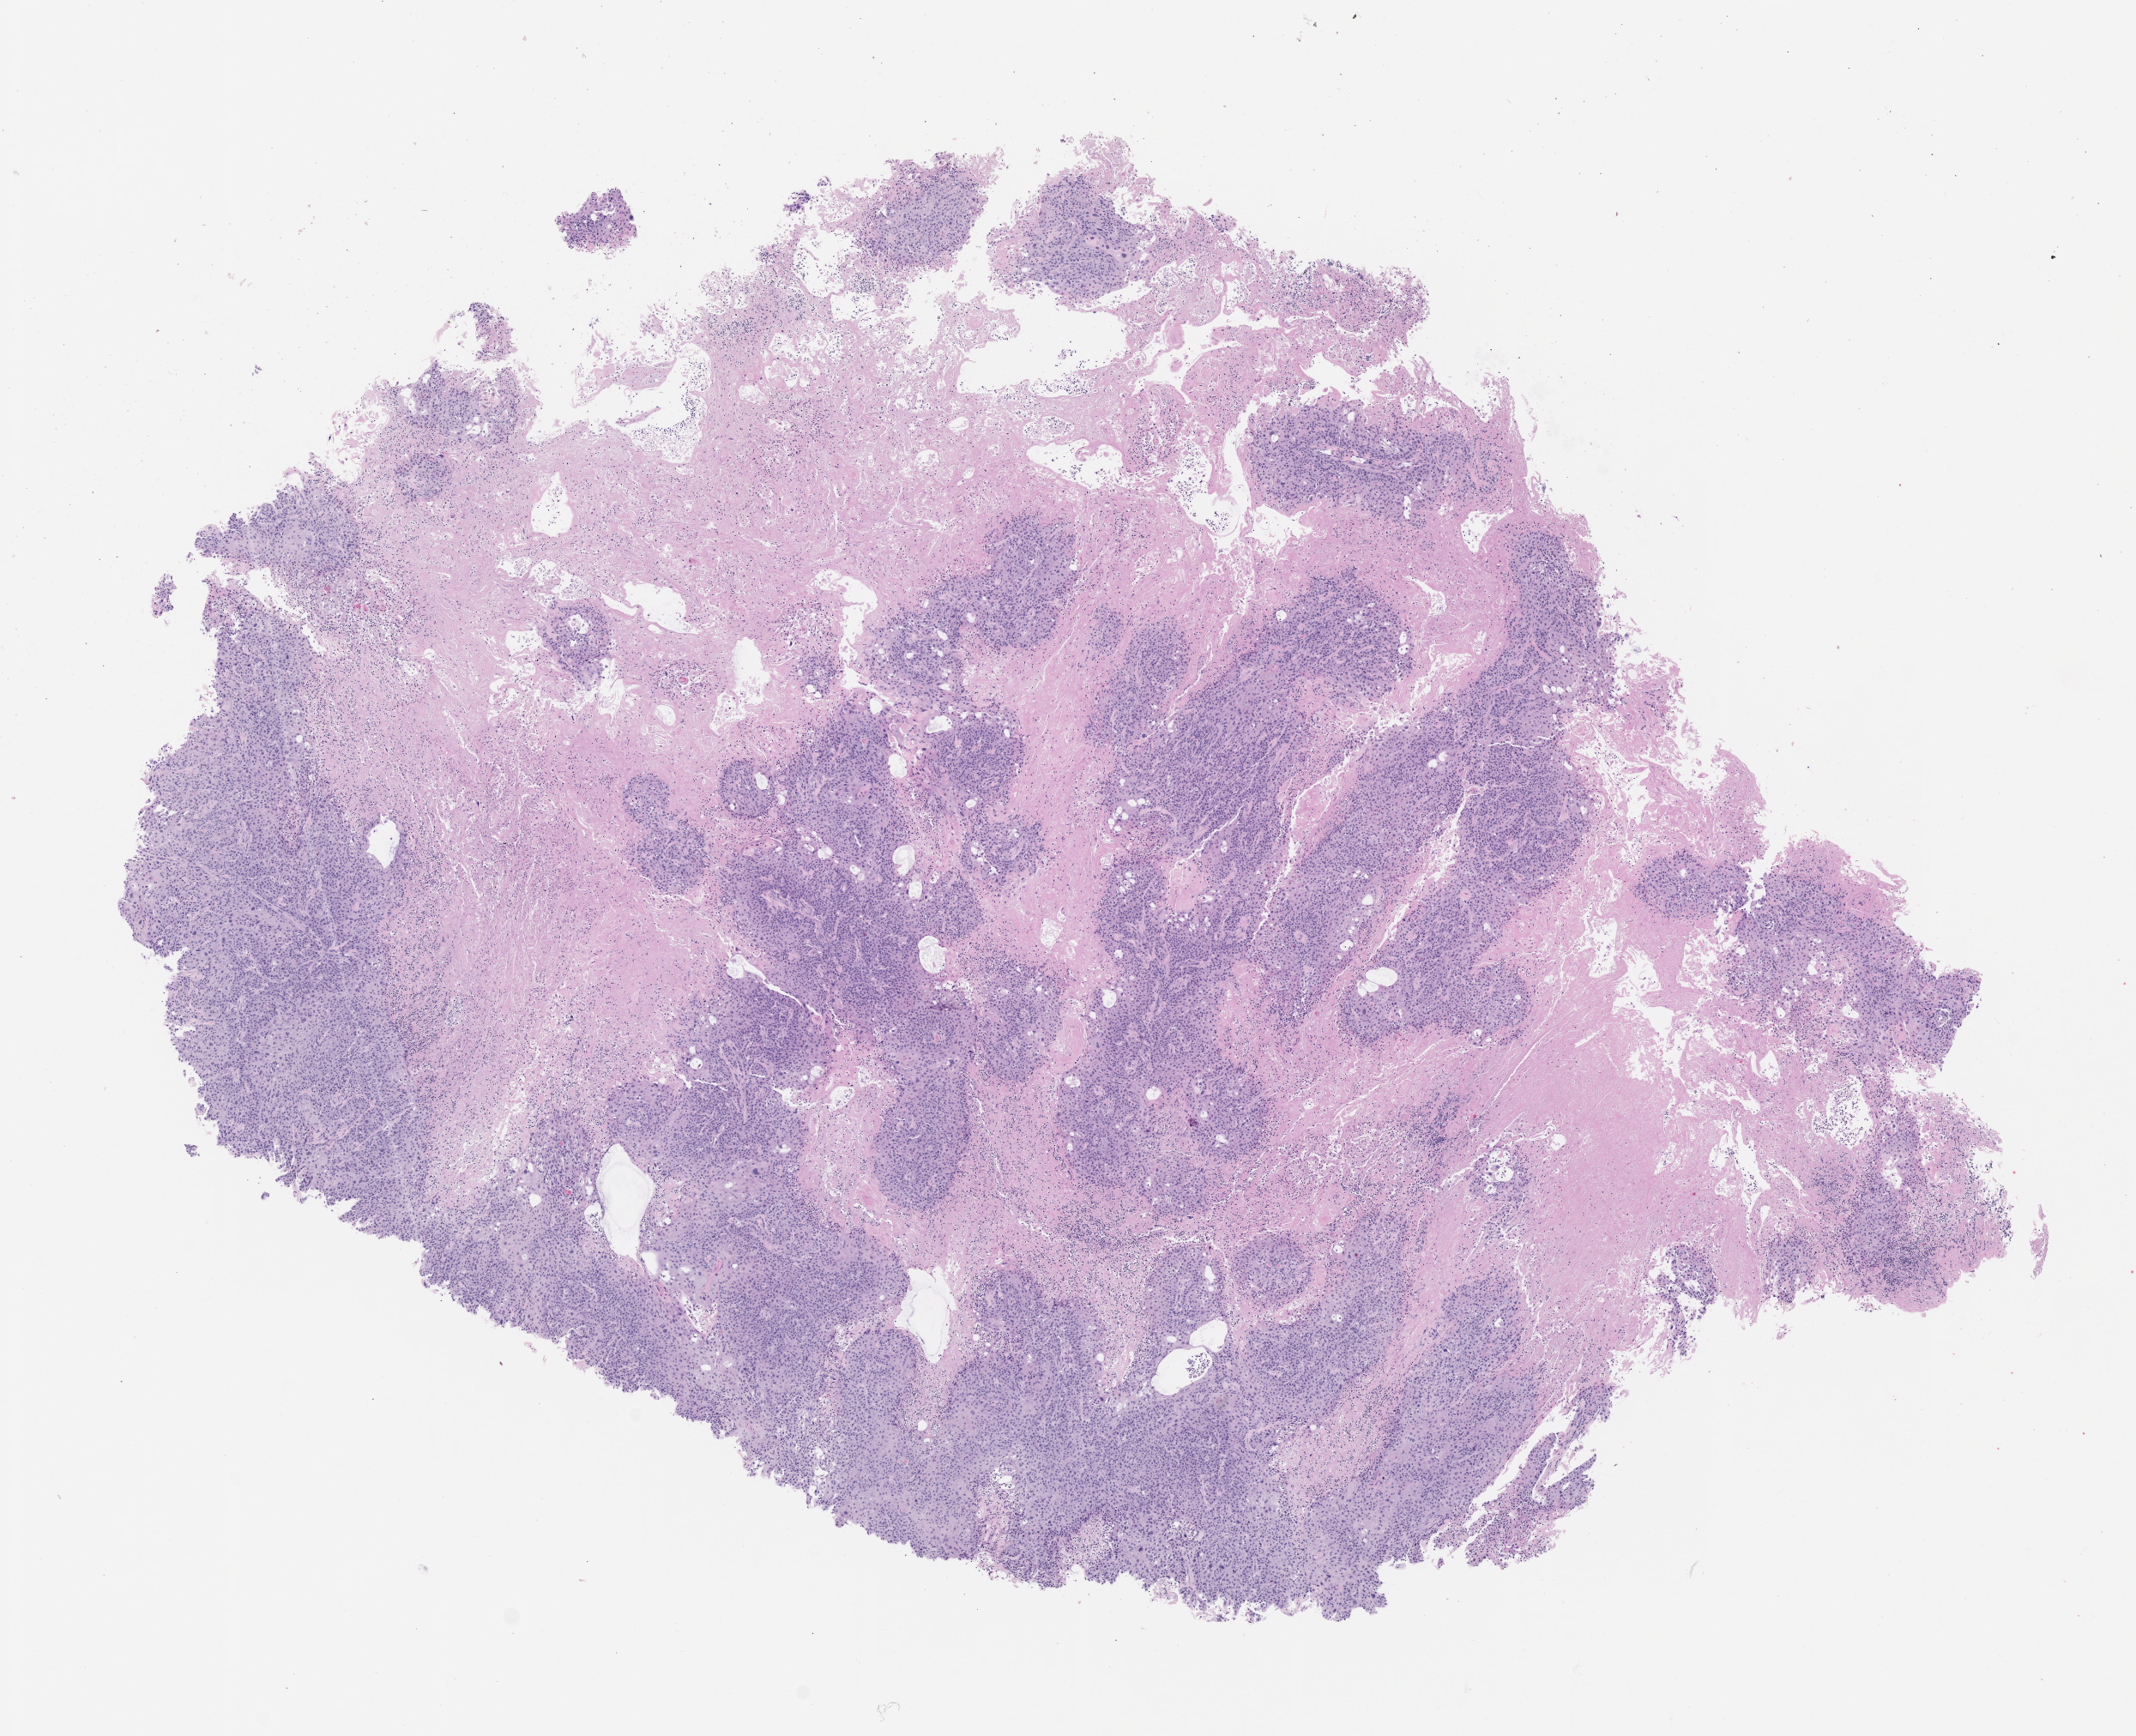
Haematoxylin and eosin whole-slide image of a patient-derived xenograft (PDX) tumor grown in a mouse, passage 1 — shown as a low-resolution overview of the whole scanned area (about 10.0 x 8.1 mm). Formalin-fixed, paraffin-embedded (FFPE) tissue. Tumor site category: head and neck.
• originating patient diagnosis: Mucoepidermoid Carcinoma